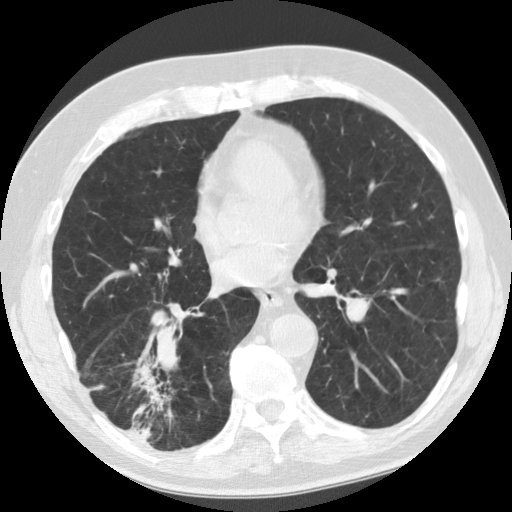
Low-dose screening chest CT, one axial slice. Position 54 of 135 along the scan axis. 120 kVp. Lung window (W 1500 / L -600 HU). 512 × 512 image matrix.
Structures marked on this image (manually delineated by an expert):
- lesion 1 (tumor, lower lobe of right lung): bounding box [x1, y1, x2, y2] px = [132, 356, 171, 417]